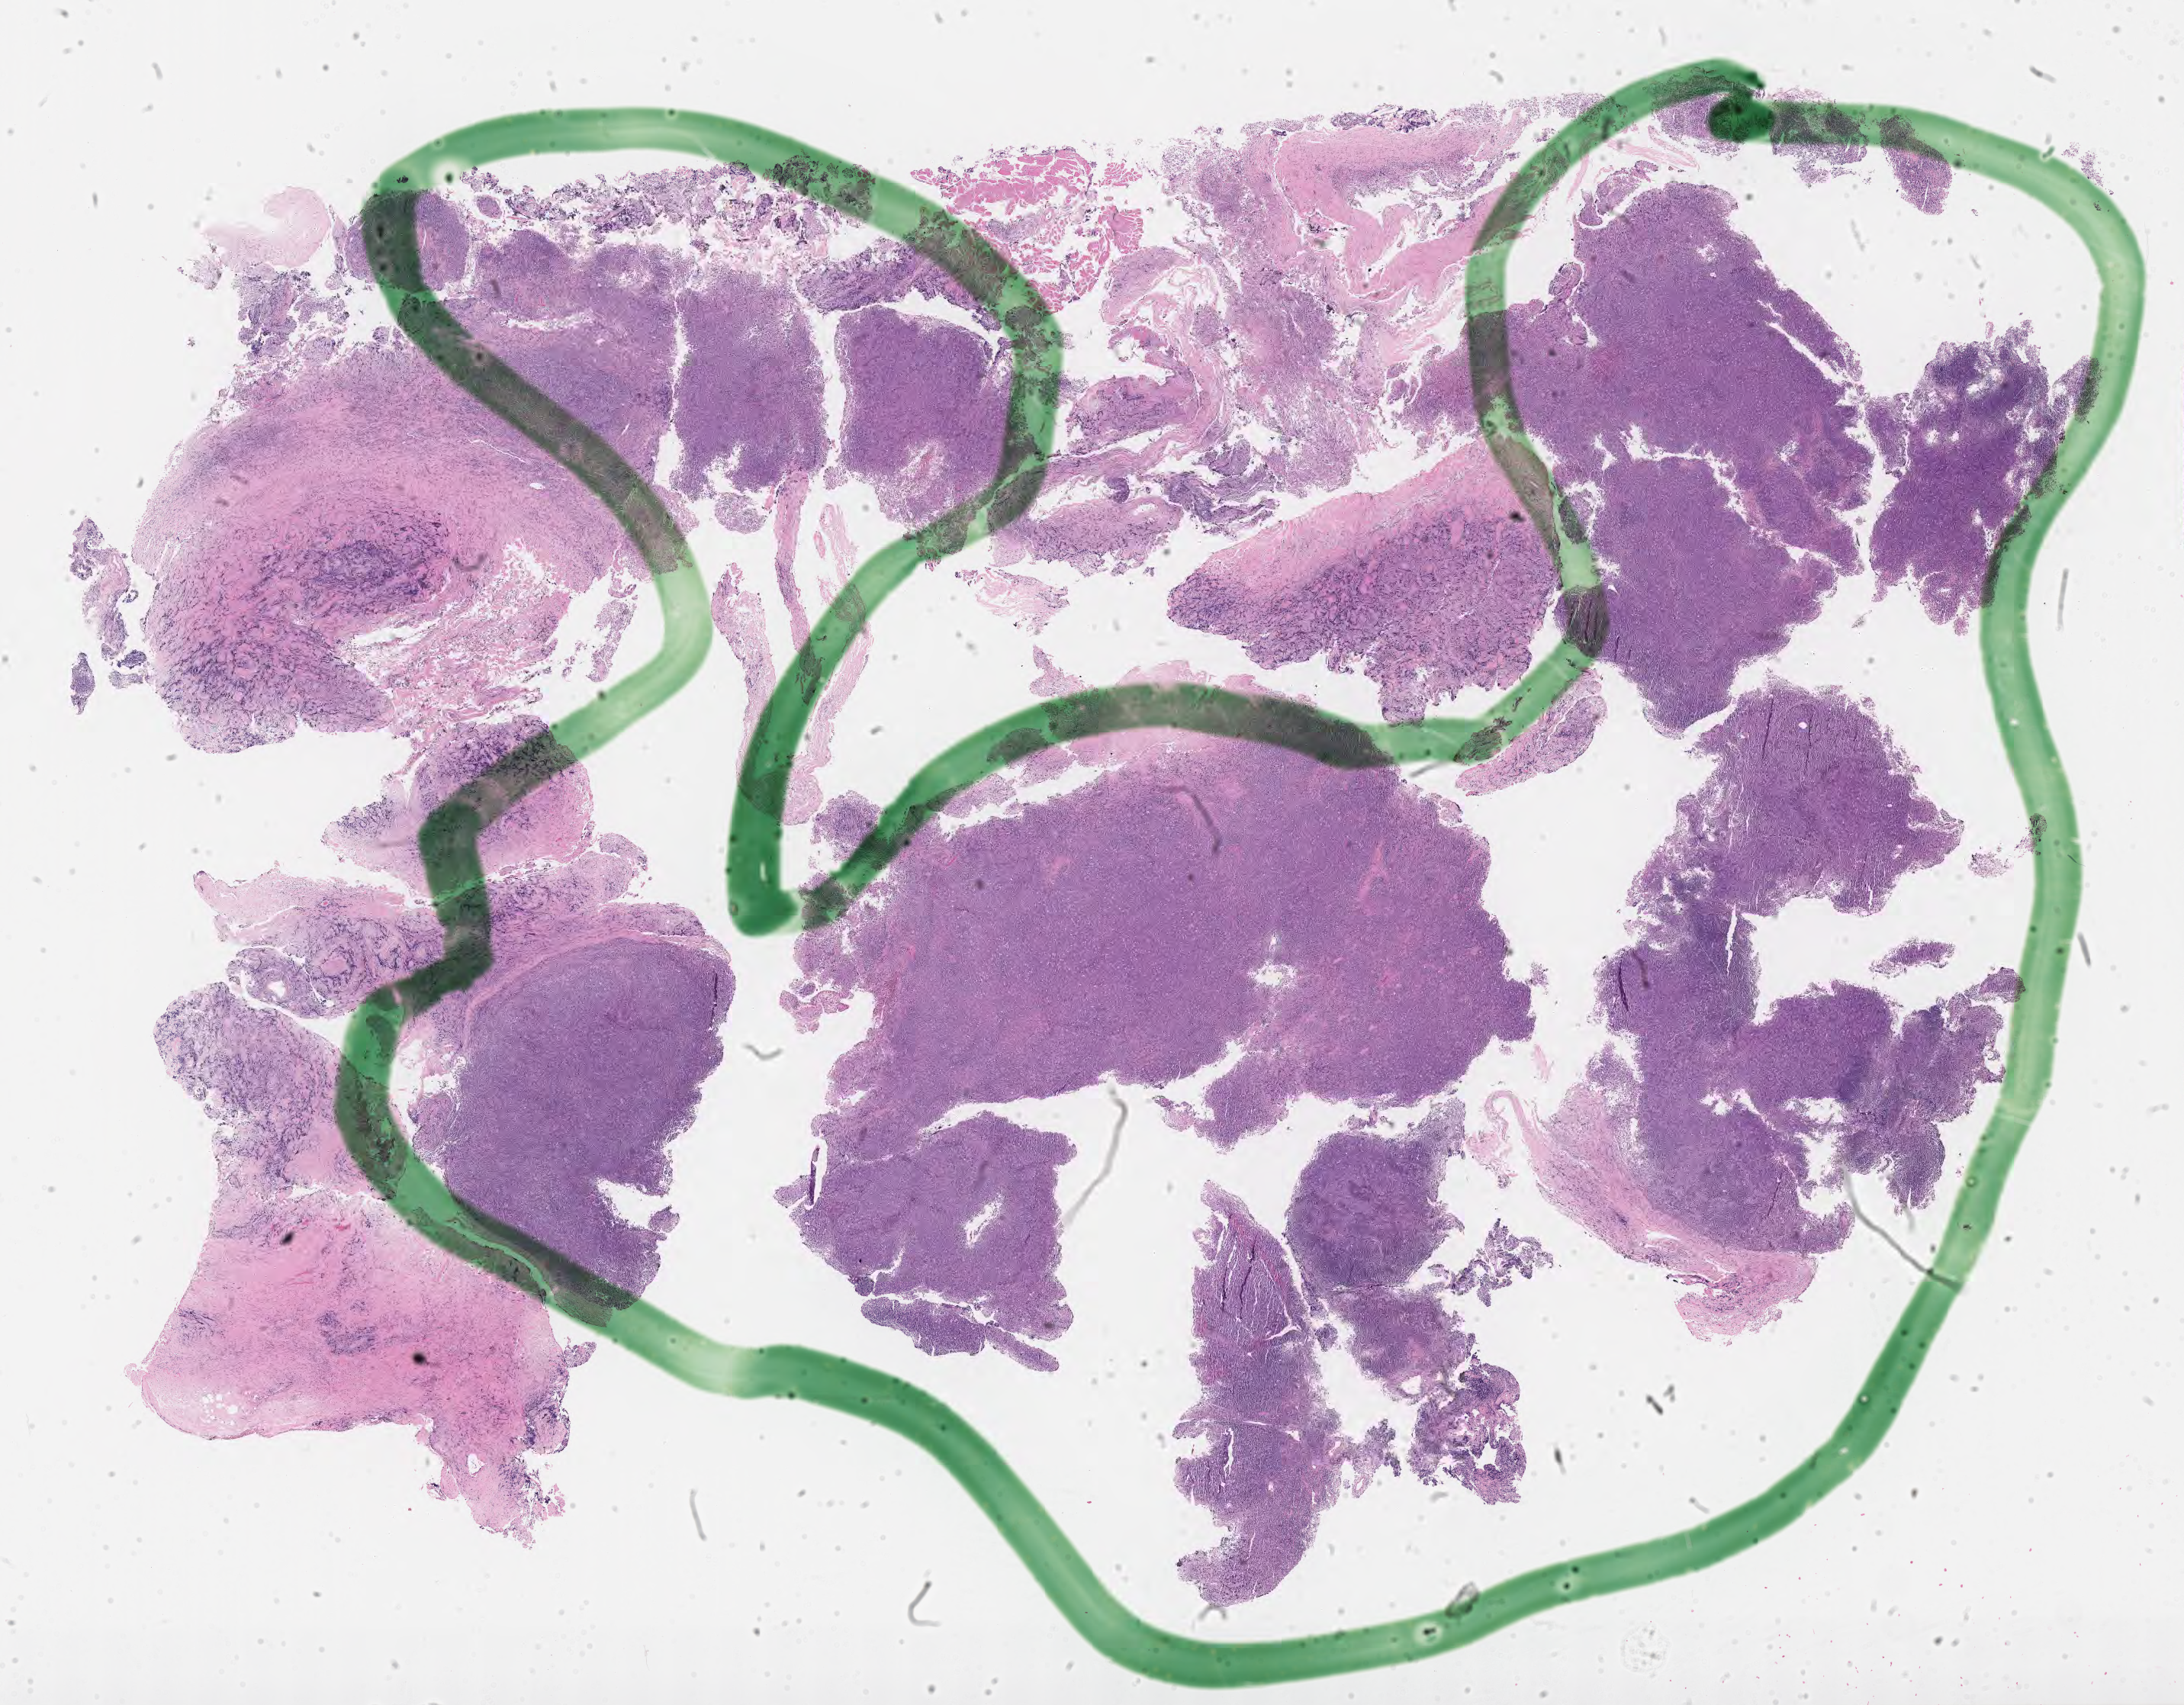
H&E whole-slide image — whole scanned area (about 23.1 x 18.1 mm) shown as a low-resolution overview; tumor tissue; site: lymph node. Male patient, 29 years old.
- histologic diagnosis: Diffuse large B-cell lymphoma, NOS